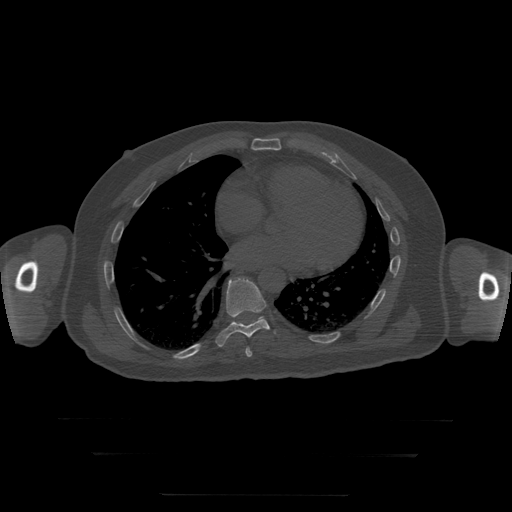
CT including the spine, one axial slice; position 144 of 397 along the scan axis; 120 kVp; bone window (W 1800 / L 400 HU); 1.25 mm slice thickness; 512 × 512 image matrix, field of view 510 × 510 mm. Patient age 73 years. From the clinical record (not read from this slice): primary cancer: prostate.
Outlined on this slice (semi-automatically segmented with operator editing):
- T10 vertebra: bounding box (x1, y1, x2, y2) in pixels: (259, 317, 264, 320)
- T8 vertebra: (246, 347, 253, 357)
- T9 vertebra: (216, 278, 276, 347)